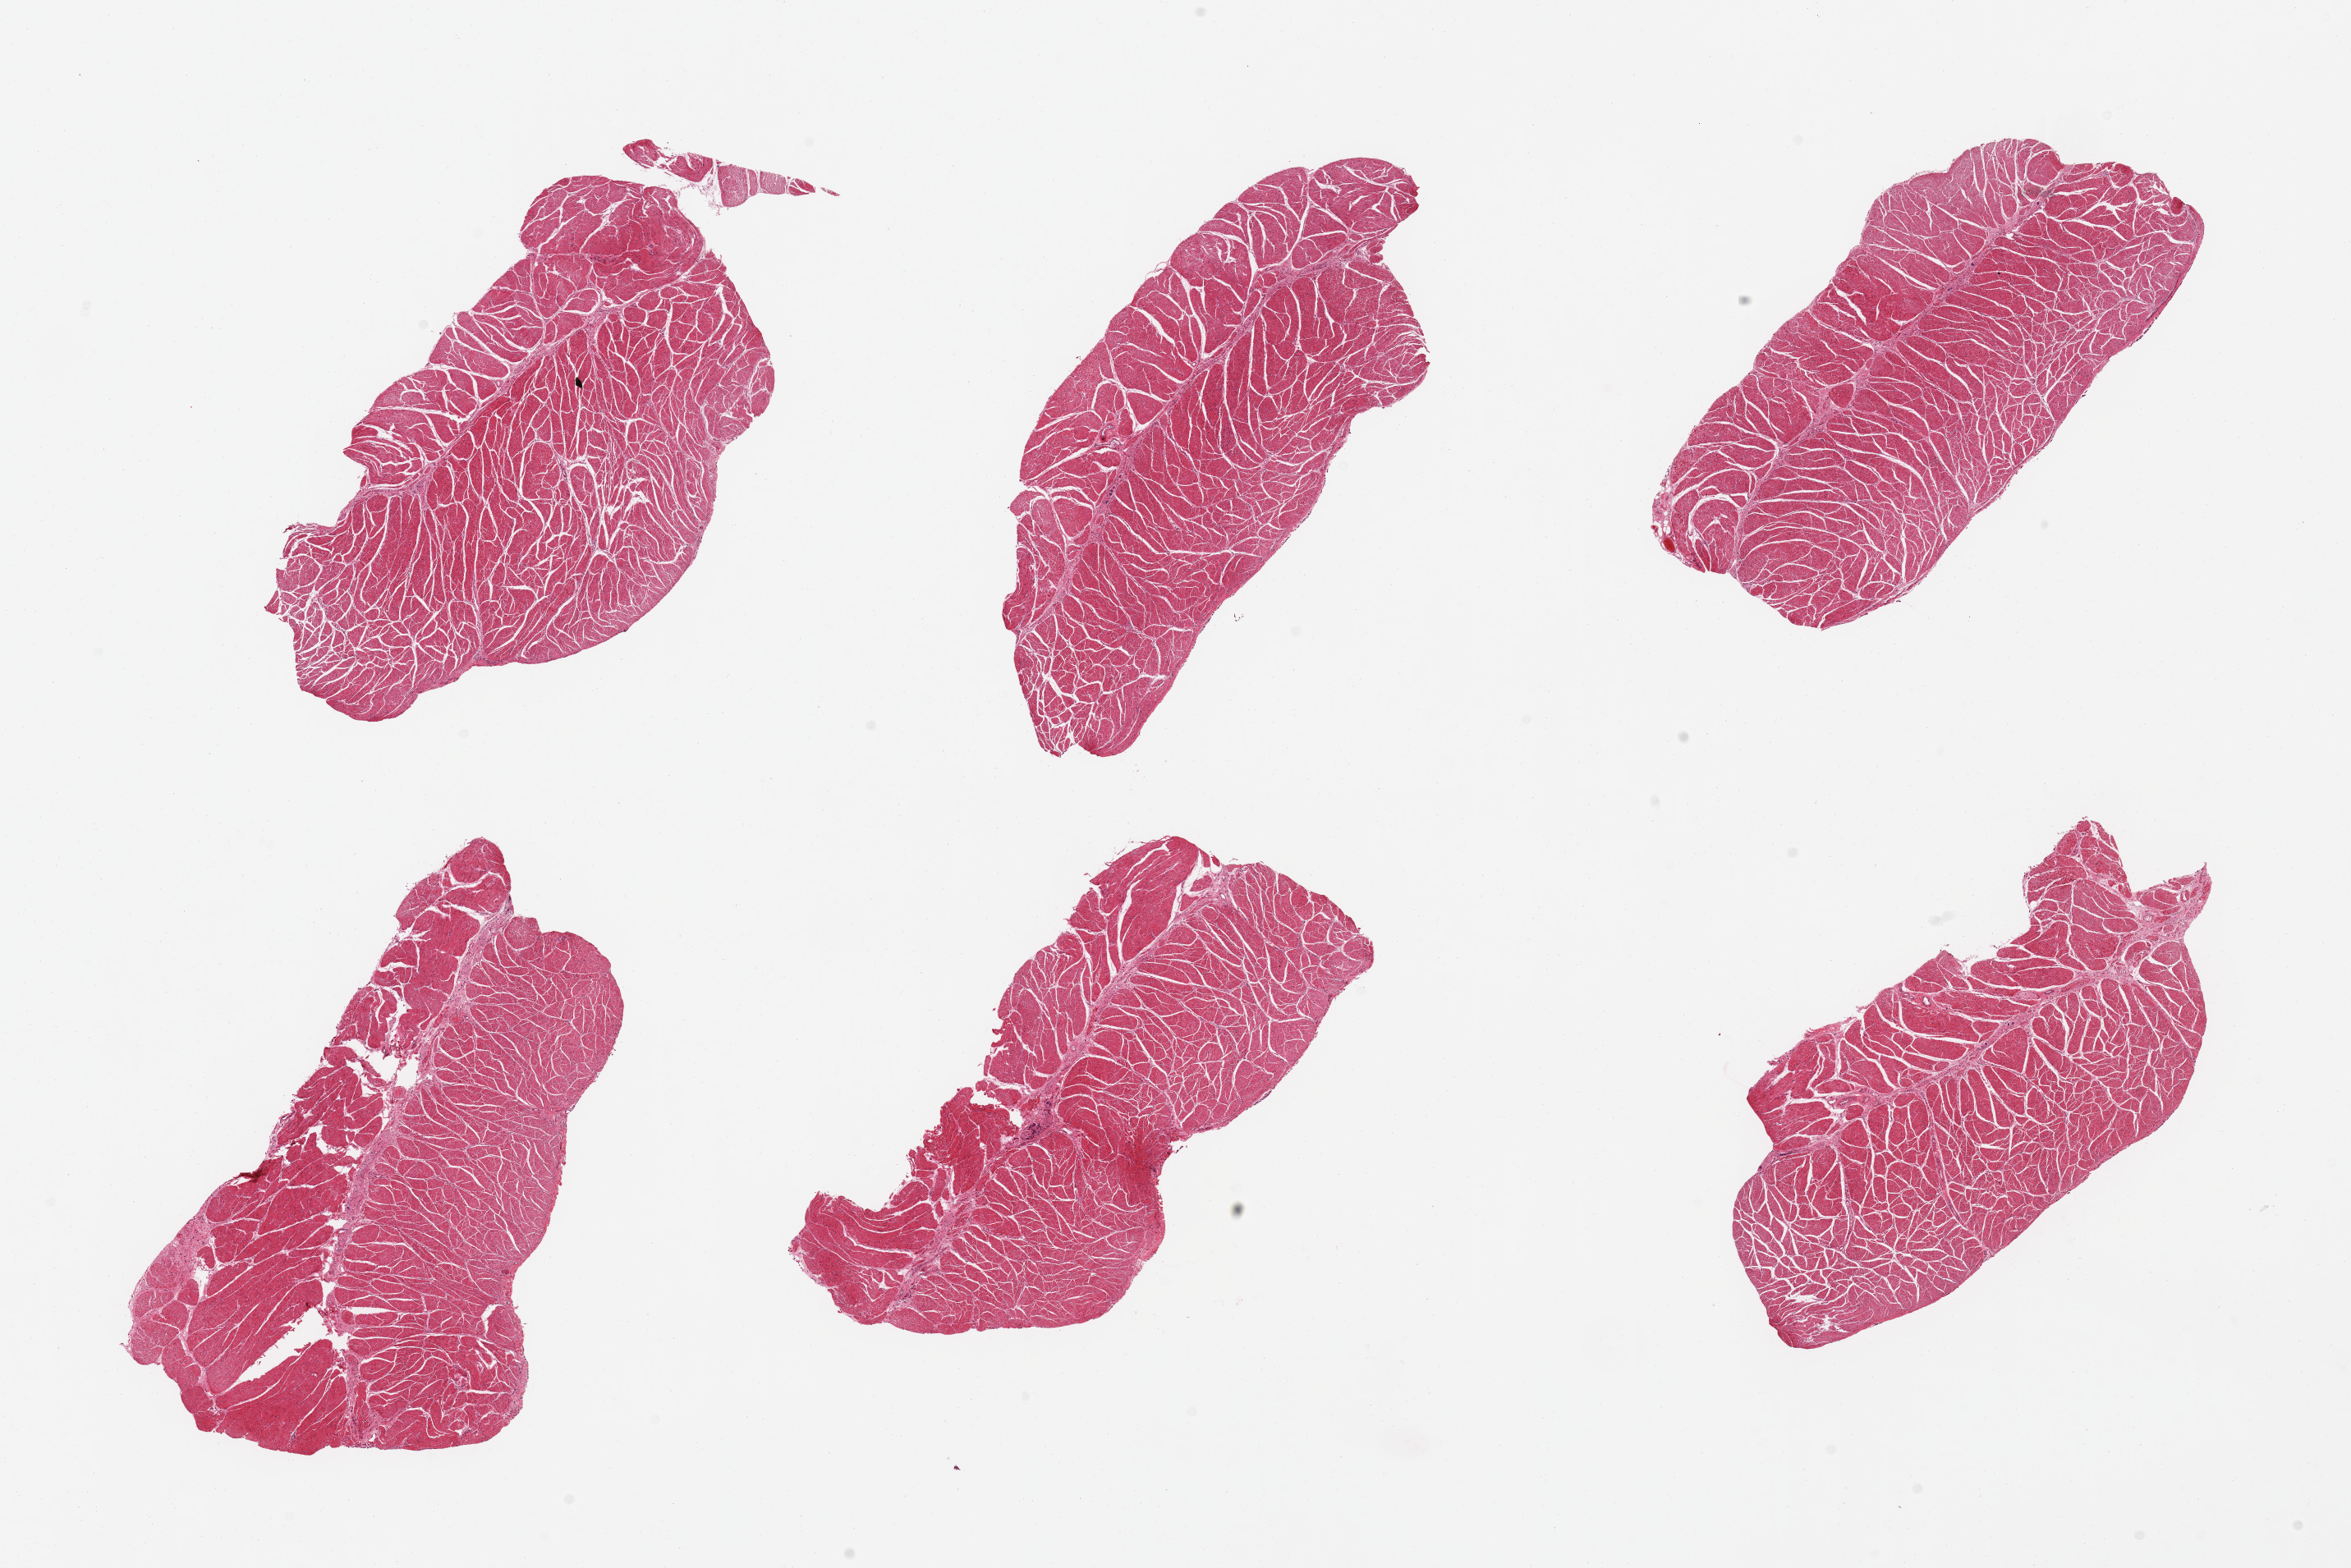
Haematoxylin and eosin whole-slide image — a low-resolution overview of the entire scanned area, about 22.6 x 15.1 mm (from a 20x scan); PAXgene-fixed paraffin-embedded (PFPE) section; section of esophageal muscle (target tissue); donor tissue sample. Male donor.
Review note (as recorded): 6 pieces, confirmed target muscularis.